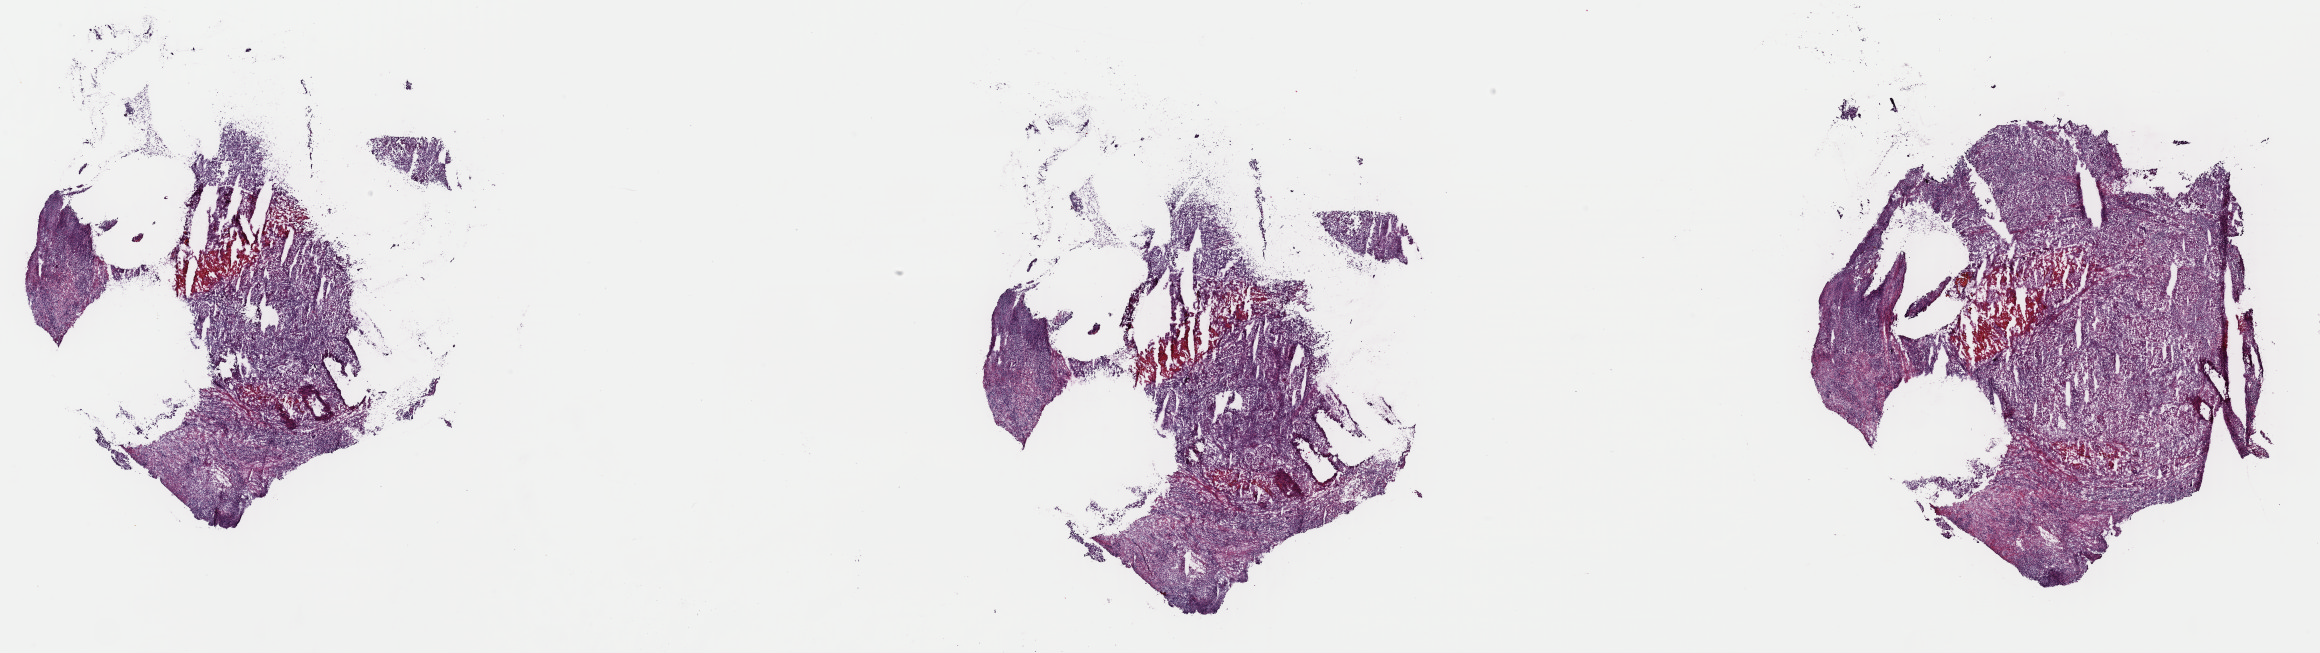
H&E whole-slide image — whole scanned area (about 36.7 x 10.3 mm, slide scanned at 40x) shown as a low-resolution overview; frozen section; sample: primary tumour, bladder. Male, age 64 years at initial diagnosis. Histologic grade: high grade. Slide review estimates, as recorded: tumour cells 70%, tumour nuclei 70%, normal cells 0%, stromal cells 25%, necrosis 5%. Infiltration values recorded for this section: lymphocyte infiltration 6%, monocyte infiltration 2%, neutrophil infiltration 3%.
TNM: T4a N1 MX. AJCC pathologic stage: IV (7th edition). Pathologic diagnosis: Transitional cell carcinoma (posterior wall of bladder).